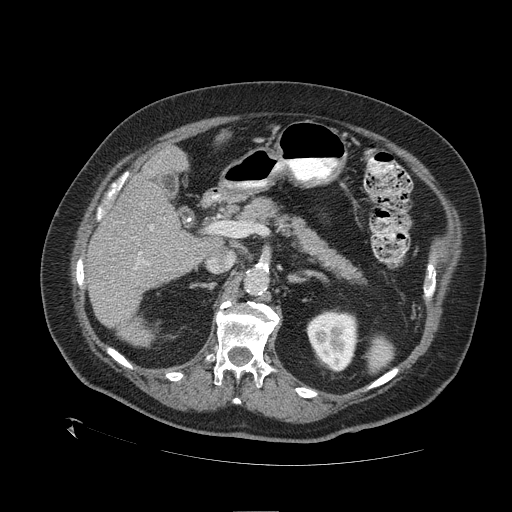
Contrast-enhanced abdominal CT (liver protocol), one axial slice; position 62 of 109 along the scan axis; 120 kVp; one of 2 acquisitions stored at this slice position; soft-tissue window (W 400 / L 40 HU); 2.5 mm slice thickness; 512 × 512 image matrix, field of view 460 × 460 mm. Case-level facts recorded for this patient, not image findings: diagnosis: hepatocellular carcinoma (patient treated with transarterial chemoembolisation; whether this scan precedes or follows treatment is not stated here); TNM stage (as recorded): Stage-I; Child-Pugh class: A; tumour differentiation: no biopsy; tumour nodularity: uninodular.
Annotated regions visible in this slice (semi-automatically segmented with operator editing):
- liver parenchyma outside the tumour (the mass and vessels are separate outlines, so this box may not span the whole liver): bounding box (x1, y1, x2, y2) in pixels: (86, 134, 227, 344)
- liver vessels: (134, 225, 153, 269)